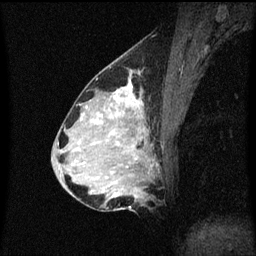
Breast MRI (dynamic contrast-enhanced), one sagittal slice. Slice 28 of 60 in the series (ordered by position). Dynamic contrast-enhanced series, image 2 of 3 at this slice position (ordered by acquisition). 1.5 T. TE 4.2 ms, TR 8.4 ms. 256 × 256 image matrix. Patient: female, 34 years. Case-level facts recorded for this patient, not image findings: setting: breast cancer imaged before/during neoadjuvant chemotherapy; receptor status: HR-positive, HER2-negative.
Annotated regions visible in this slice (semi-automatic segmentation, software-assisted and operator-edited):
- analysis volume of interest (the breast-tissue region the enhancement analysis was run in; not a lesion): bounding box (x1, y1, x2, y2) in pixels: (69, 70, 159, 209)
- tumour enhancement mask (voxels above the 70 % enhancement threshold inside the analysis volume of interest): (110, 84, 142, 197)